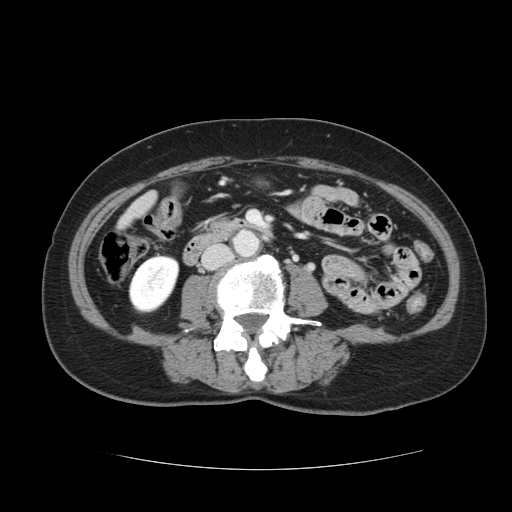
Contrast-enhanced abdominal CT, one axial slice. Slice 13 of 128 in the series (ordered by position). 120 kVp. Intravenous contrast given. Soft-tissue window (W 400 / L 40 HU). 2.5 mm slice thickness. 512 × 512 image matrix. Female patient, age 67 years. Case-level facts recorded for this patient, not image findings: diagnosis: colorectal cancer liver metastases, imaged before liver resection; multiple liver metastases: yes; largest metastasis: 3 cm; disease in both lobes: yes.
Structures marked on this image (manually delineated by an expert):
- liver: bounding box (x1, y1, x2, y2) in pixels: (124, 195, 155, 223)
- planned liver remnant (the part of the liver to remain after resection): (124, 207, 141, 223)